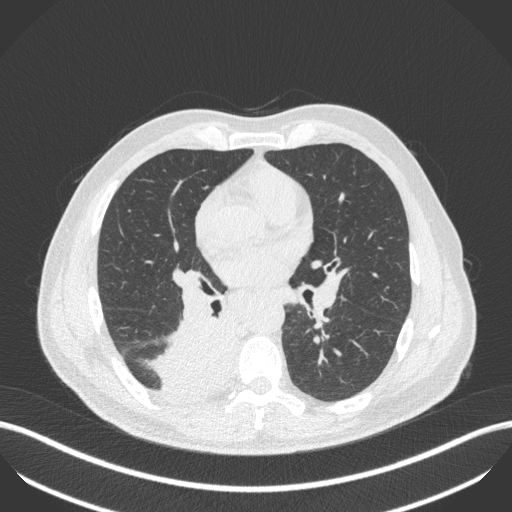
Chest CT, one axial slice; slice 248 of 451 in the series (ordered by position); 100 kVp; lung window (W 1500 / L -600 HU); 1 mm slice thickness; 512 × 512 image matrix. Patient: male, 61 years. From the clinical record (not read from this slice): clinical TNM (as recorded): T1 N0 M0.
Structures marked on this image (bounding box drawn by a radiologist):
- lung tumour (recorded histology: small cell carcinoma): bounding box (x1, y1, x2, y2) in pixels: (148, 313, 246, 408)